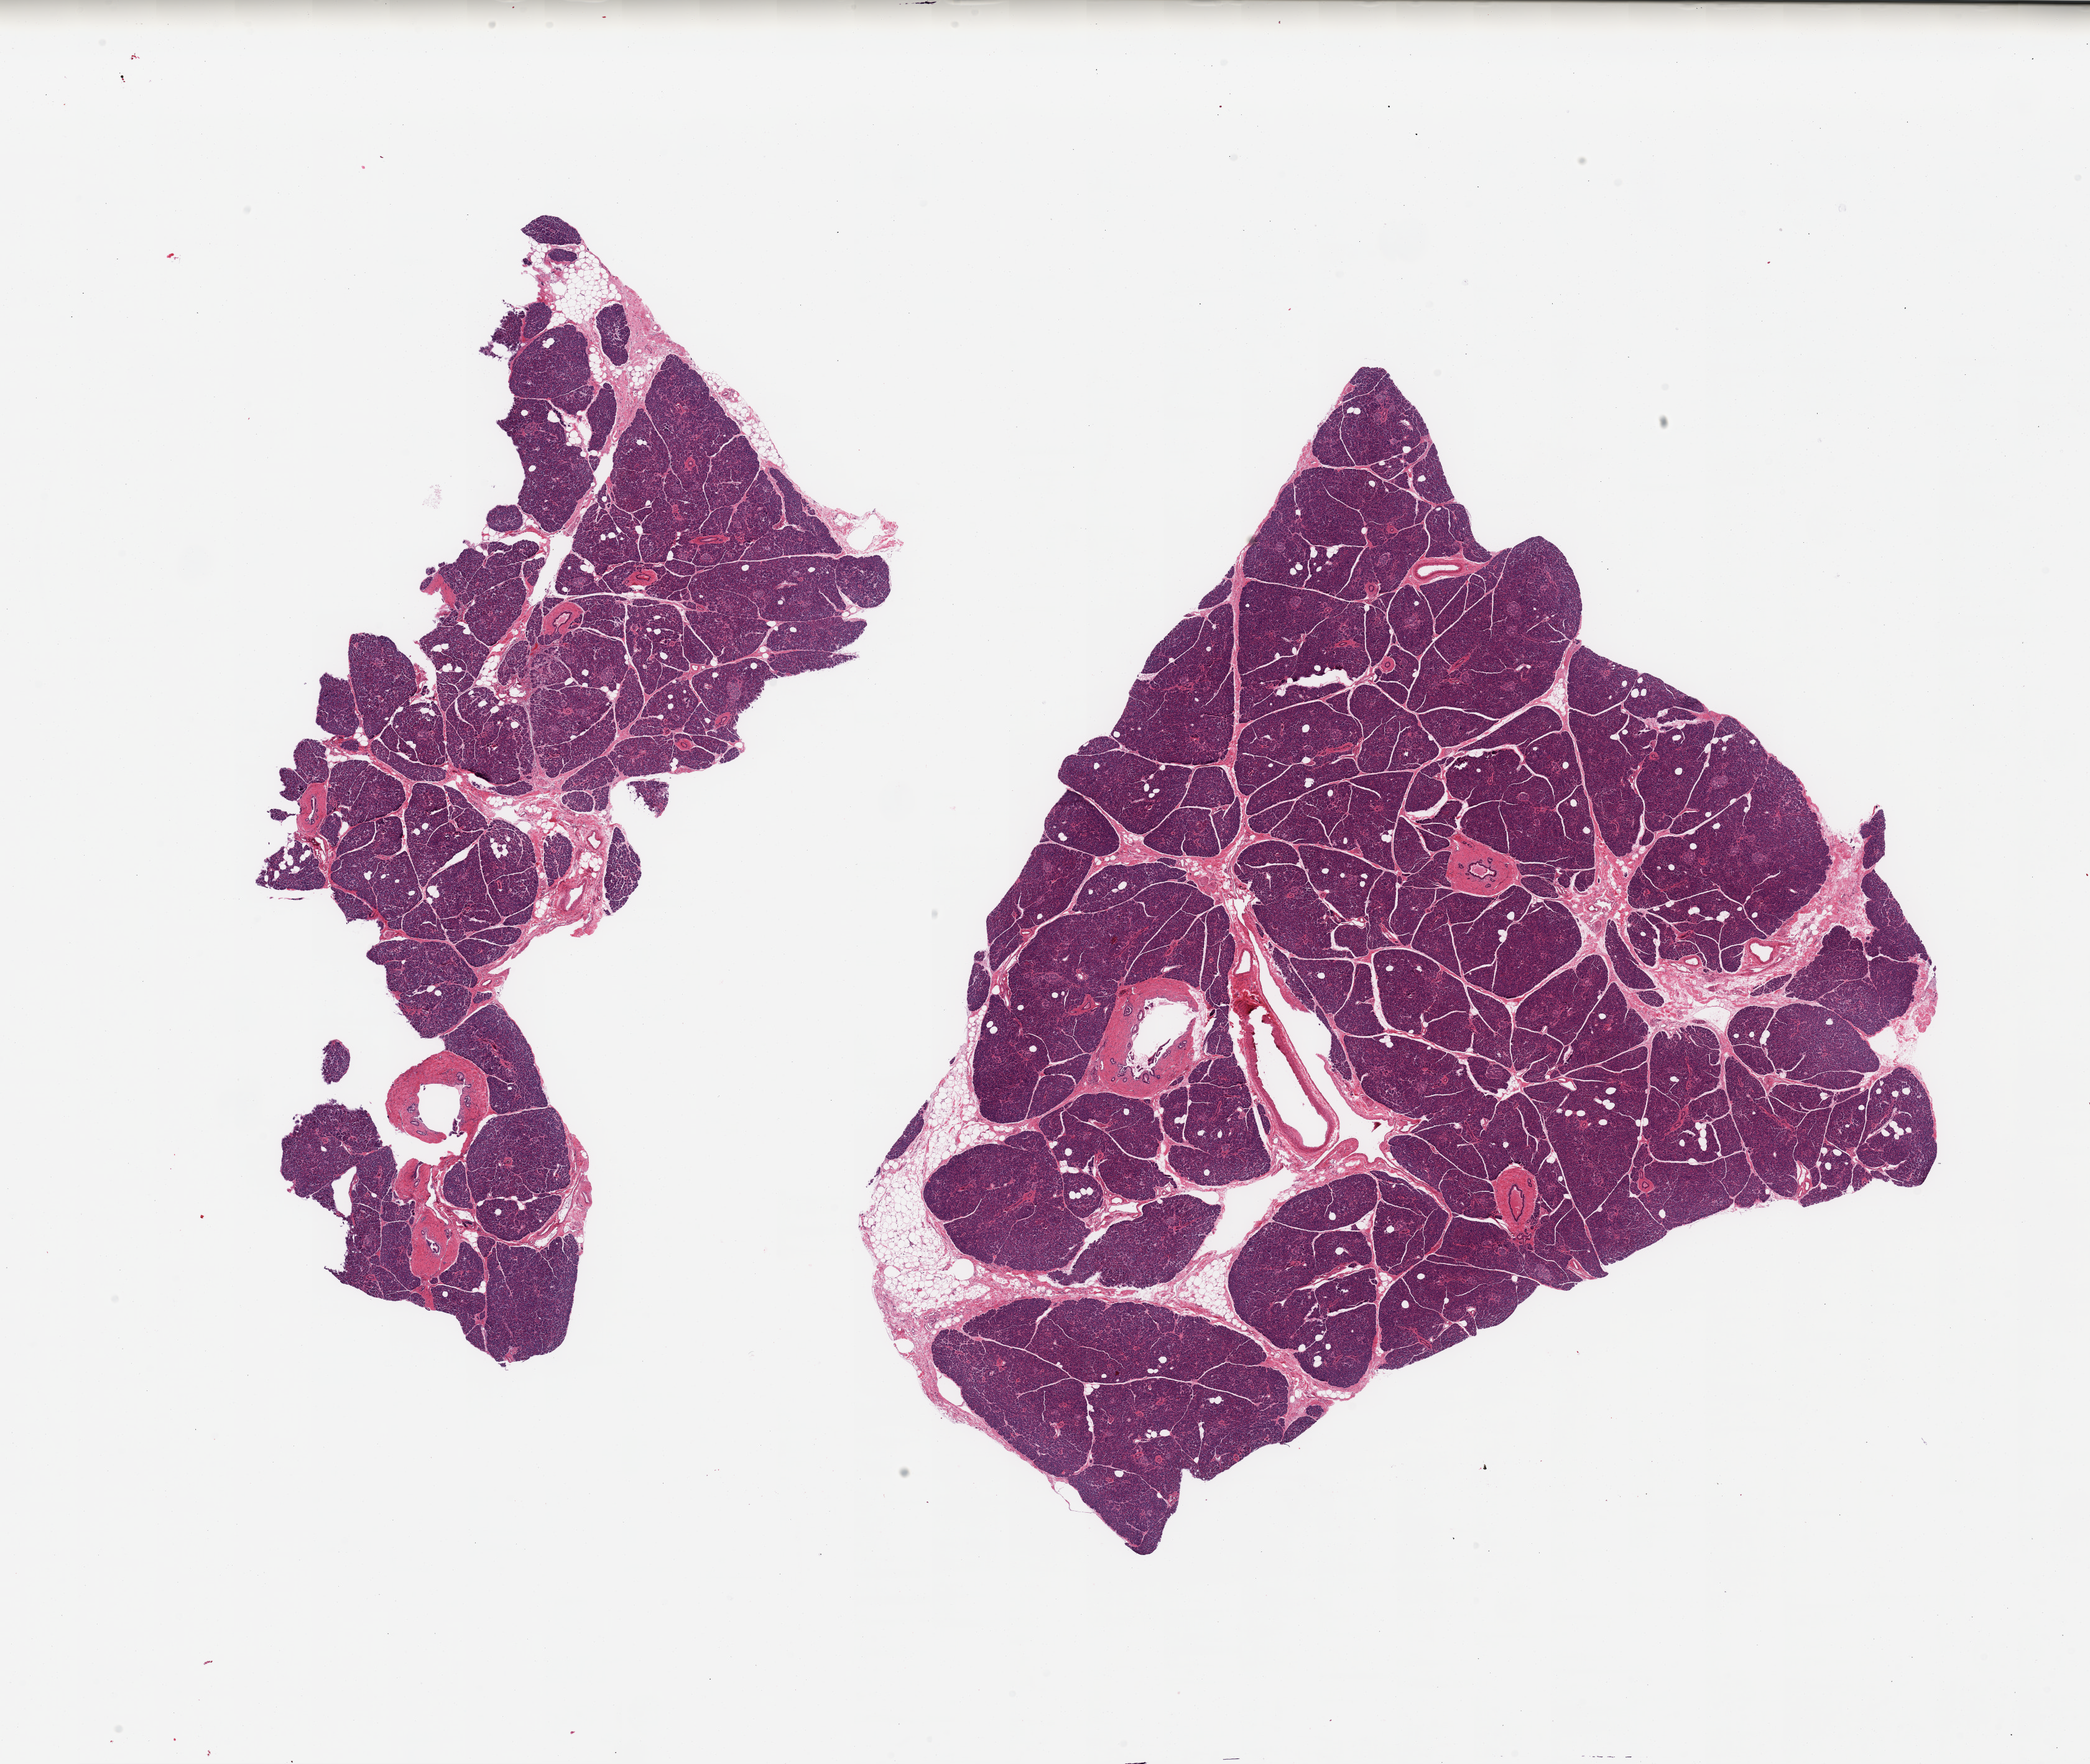
Digitized H&E-stained section — low-resolution overview of the scanned area, about 26.6 x 22.4 mm (slide scanned at 20x), PAXgene-fixed, paraffin-embedded tissue, section of pancreas (target tissue), tissue donor sample.
Pathologist's review note for this sample: 2 pieces; well preserved parenchyma with Langerhans islets; accentuation of periductal connective tissue; mild to moderate autolysis of septal fat.